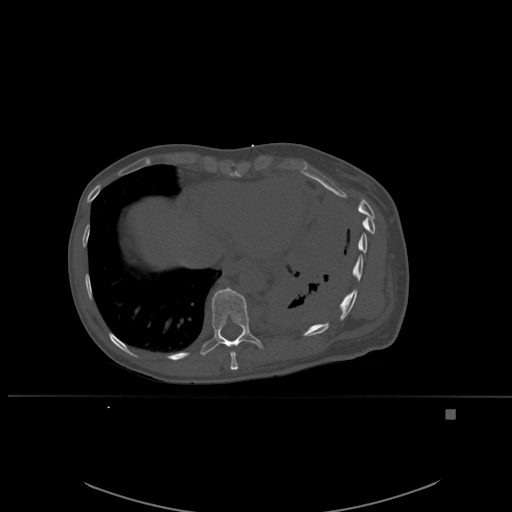
CT including the spine, one axial slice. Position 320 of 537 along the scan axis. Bone window (W 1800 / L 400 HU). 1.5 mm slice thickness. 512 × 512 image matrix, field of view 440 × 440 mm. Patient: female, 45 years. From the clinical record (not read from this slice): primary cancer: lung.
Structures marked on this image (semi-automatic segmentation, software-assisted and operator-edited):
- T10 vertebra: bounding box (x1, y1, x2, y2) in pixels: (200, 287, 263, 356)
- T9 vertebra: (230, 351, 238, 370)